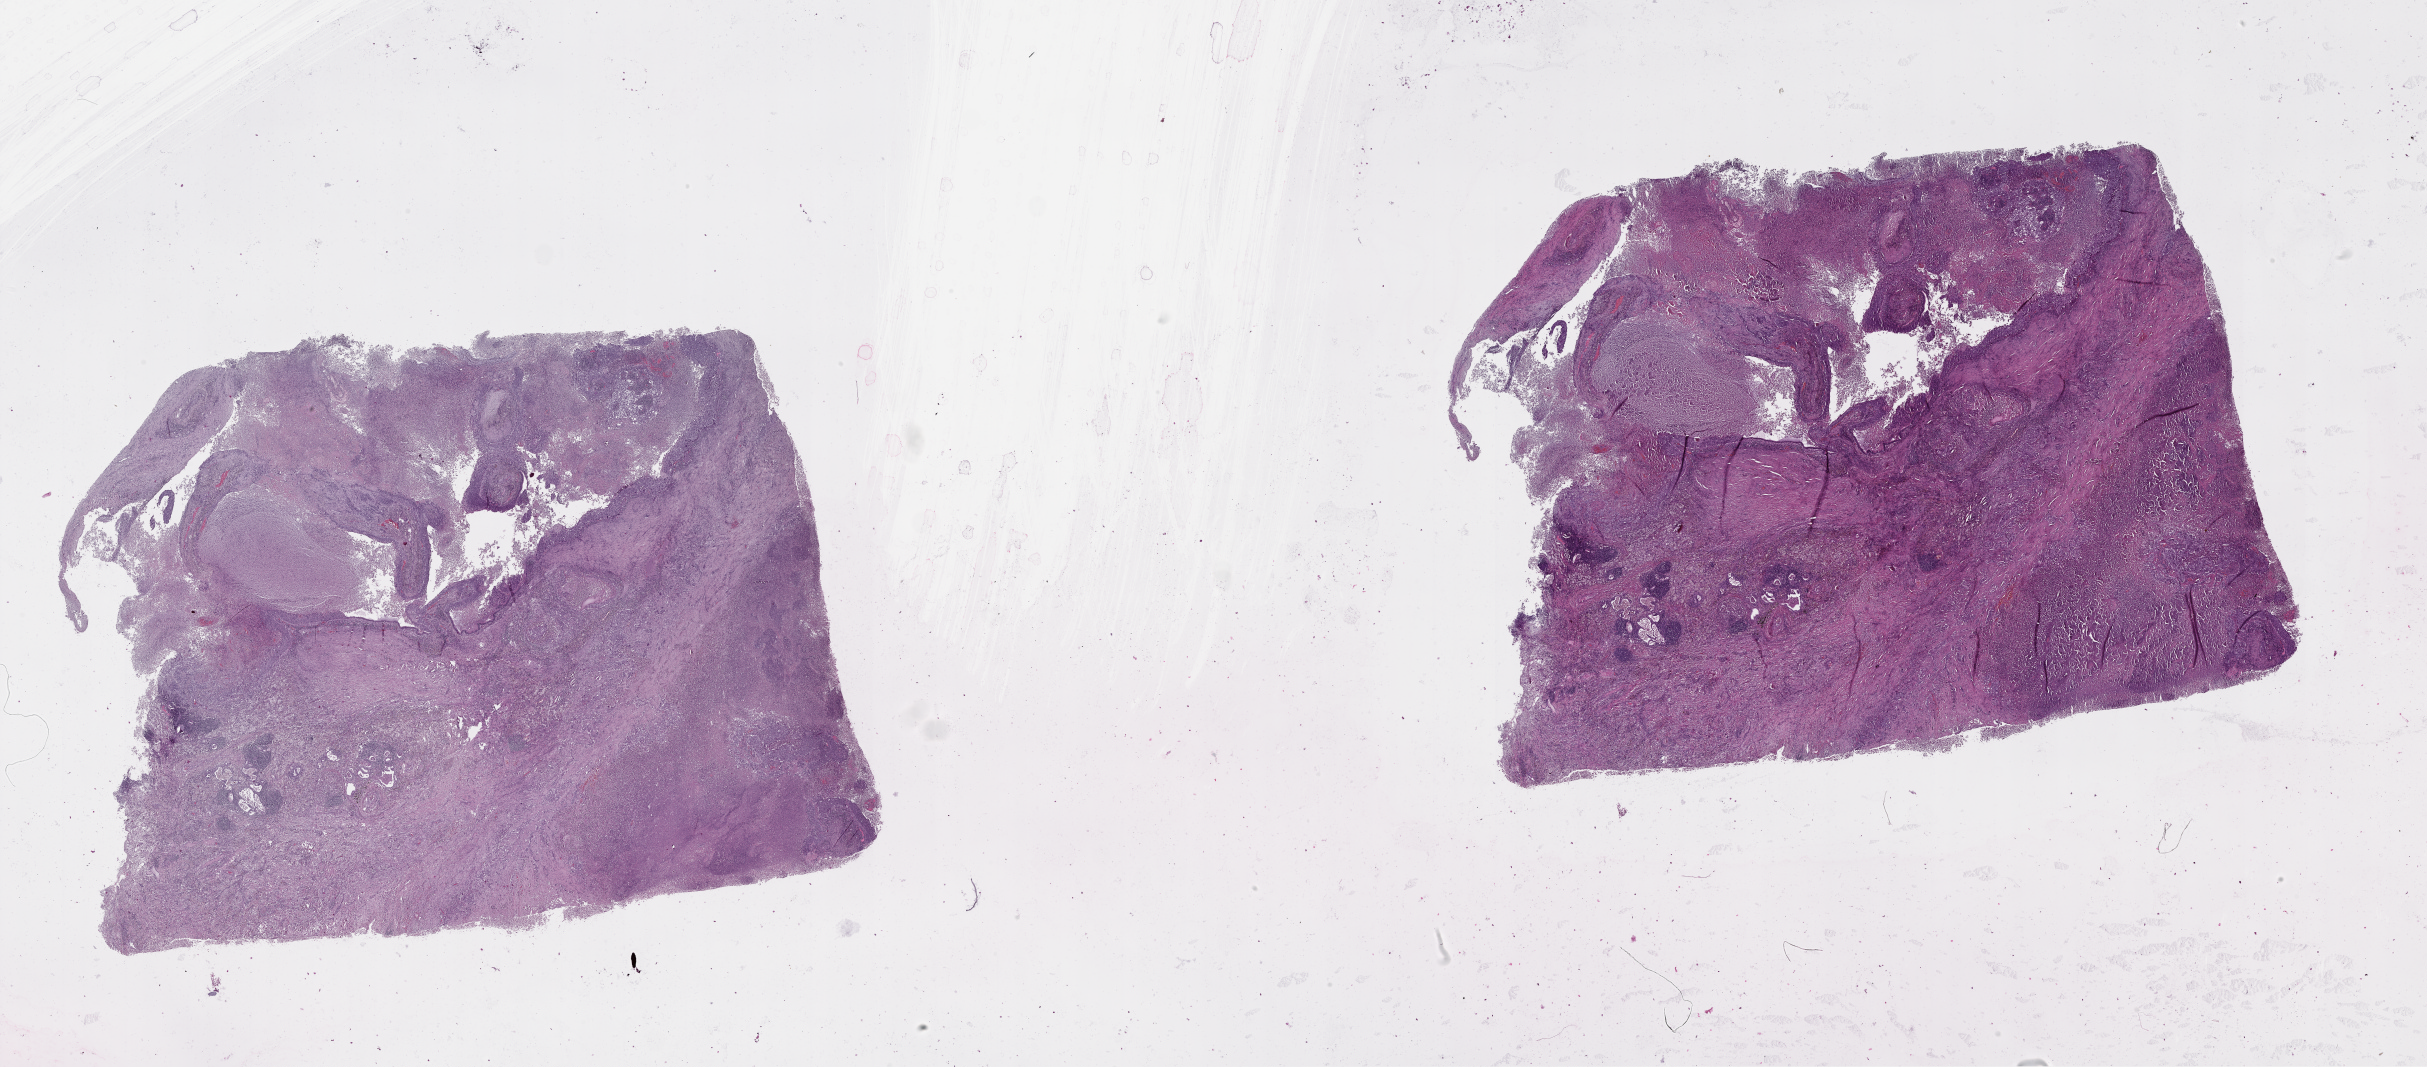
H&E whole-slide image, shown as a low-resolution overview of the whole scanned area (about 39.1 x 17.2 mm, acquisition: 20x scan); lung, tumour tissue. Patient: male, age 67 years.
• patient diagnosis (cohort enrolment): squamous cell carcinoma (lung)